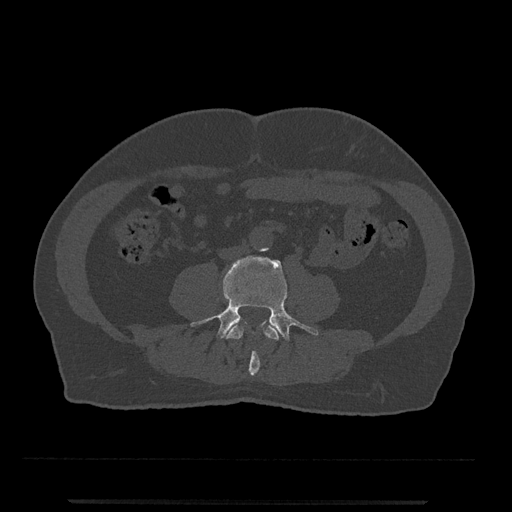
CT including the spine, one axial slice. Position 157 of 797 along the scan axis. Reconstruction kernel Br40s/3. Bone window (W 1800 / L 400 HU). 0.5 mm slice thickness. 512 × 512 image matrix, field of view 419 × 419 mm. Male patient, age 63 years. Case-level facts recorded for this patient, not image findings: primary cancer: prostate.
Structures marked on this image (semi-automatically segmented with operator editing):
- L3 vertebra: bounding box [x1, y1, x2, y2] px = [227, 323, 281, 376]
- L4 vertebra: [190, 256, 319, 341]